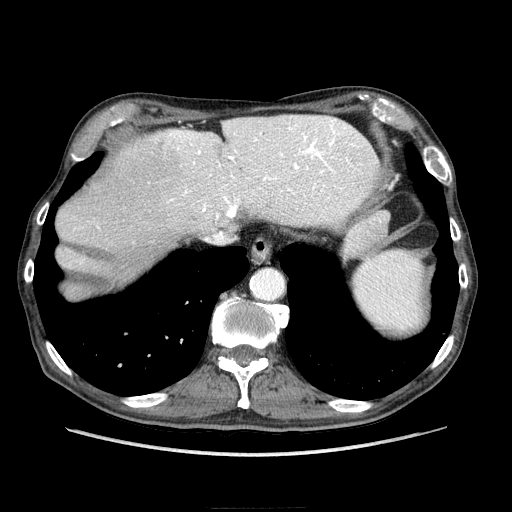
Contrast-enhanced abdominal CT (liver protocol), one axial slice. Position 185 of 218 along the scan axis. Reconstruction kernel STANDARD. Soft-tissue window (W 400 / L 40 HU). 2.5 mm slice thickness. 512 × 512 image matrix, field of view 380 × 380 mm. From the clinical record (not read from this slice): diagnosis: hepatocellular carcinoma (patient treated with transarterial chemoembolisation; whether this scan precedes or follows treatment is not stated here); TNM stage (as recorded): Stage-IIIA; Child-Pugh class: A; tumour nodularity: multinodular.
Structures marked on this image (semi-automatically segmented with operator editing):
- liver parenchyma outside the tumour (the mass and vessels are separate outlines, so this box may not span the whole liver): bounding box <110,114,378,260> (left, top, right, bottom; pixels)
- liver vessels: <155,116,377,221>